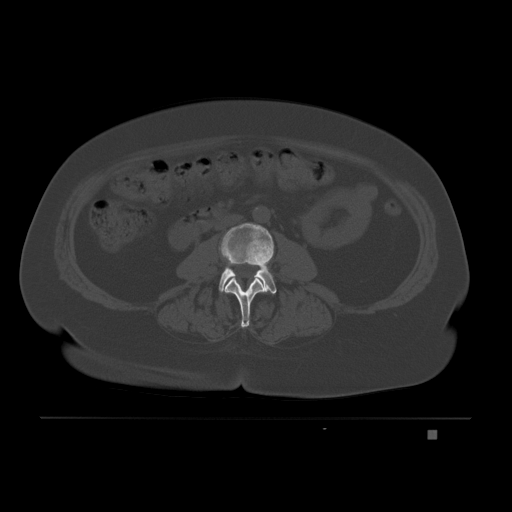
CT including the spine, one axial slice; slice 55 of 221 in the series (ordered by position); bone window (W 1800 / L 400 HU); 3 mm slice thickness; 512 × 512 image matrix, field of view 474 × 474 mm. Female patient, age 63 years. Case-level facts recorded for this patient, not image findings: primary cancer: breast.
Structures marked on this image (semi-automatic segmentation, software-assisted and operator-edited):
- L2 vertebra: box from (x=223, y=278) to (x=266, y=328) px
- L3 vertebra: (x=219, y=223)–(x=277, y=294)